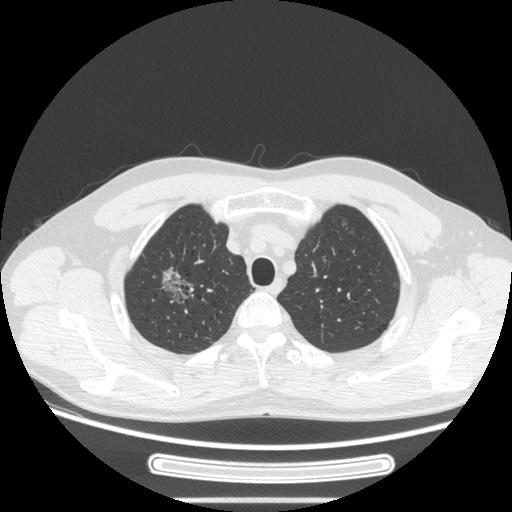
Chest CT, one axial slice; position 220 of 269 along the scan axis; reconstruction kernel STANDARD; 120 kVp; lung window (W 1500 / L -600 HU); 1.25 mm slice thickness; 512 × 512 image matrix. Patient: male, 53 years. Case-level facts recorded for this patient, not image findings: clinical TNM (as recorded): T1c N0 M0; histopathological grade: G2.
Outlined on this slice (rectangle marked by the reading radiologist):
- lung tumour (recorded histology: adenocarcinoma): box from (x=154, y=261) to (x=196, y=312) px